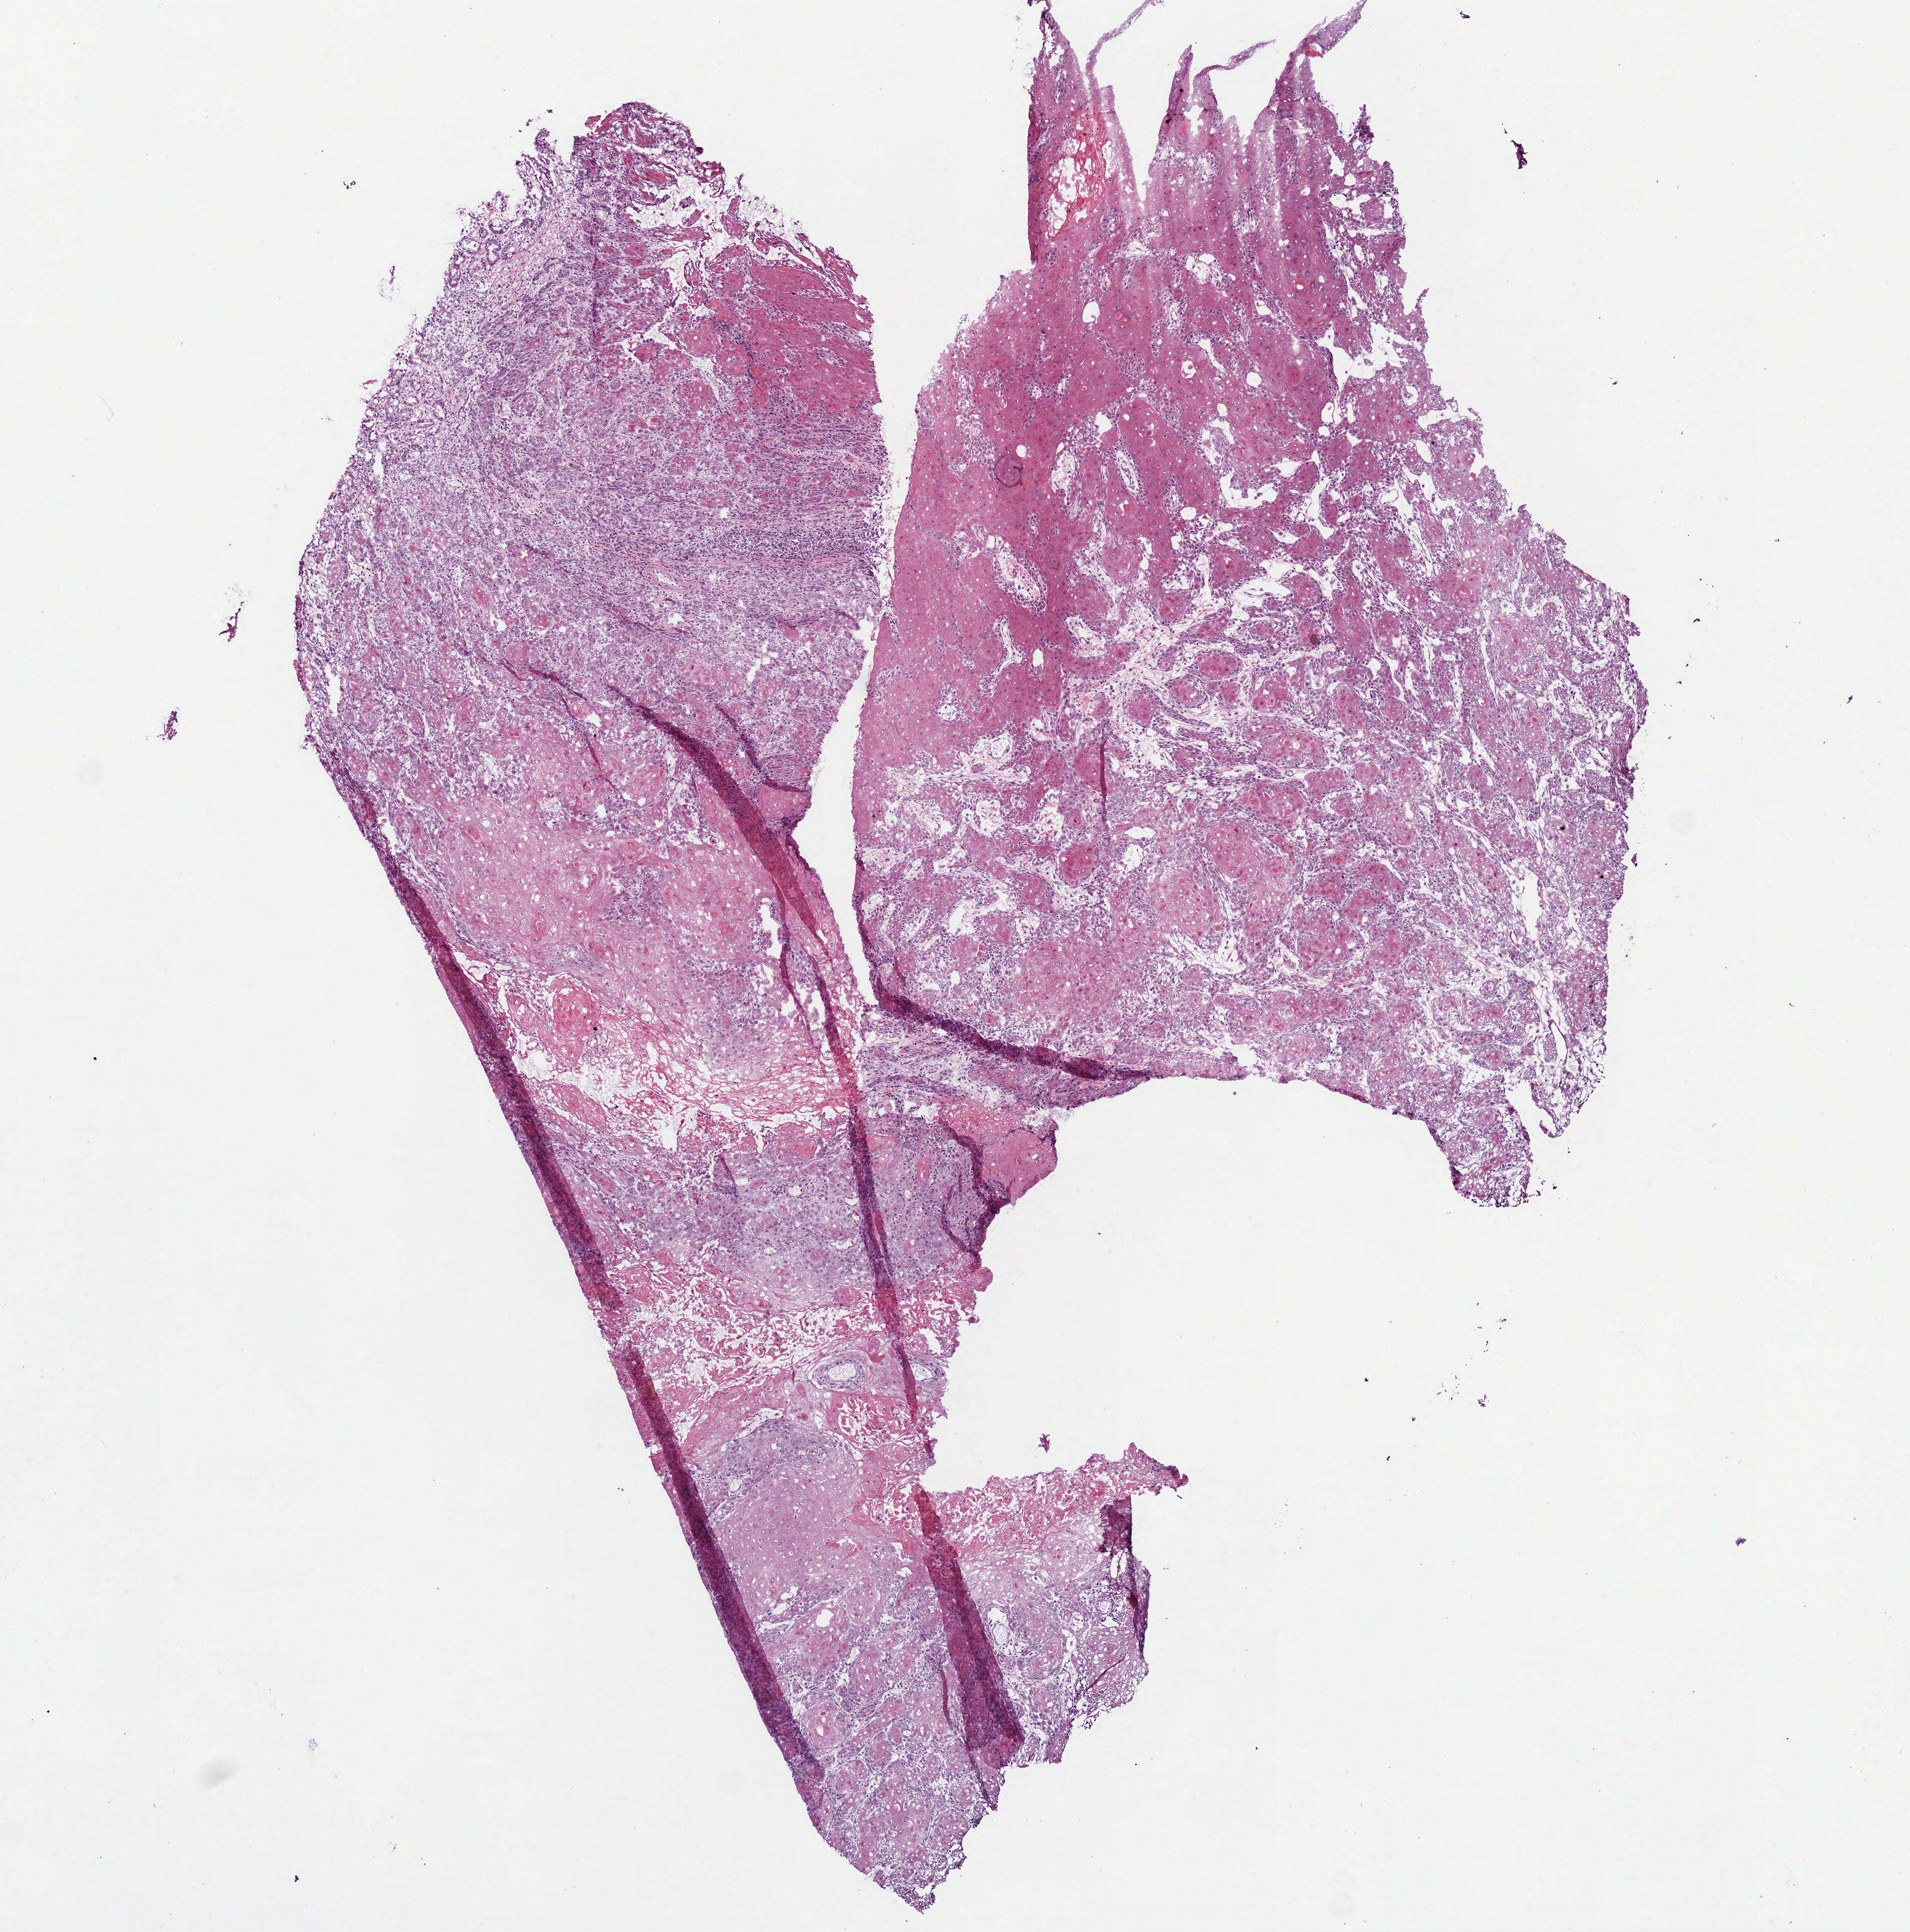
Whole-slide histology image, H&E-stained, low-resolution overview of the scanned area, about 6.0 x 6.1 mm; frozen section; head and neck, primary tumour sample. Female, age 52 years at initial diagnosis. Histologic grade: G2 (moderately differentiated). Pathologist review of this section (percent, as recorded): tumour cells 88%, tumour nuclei 80%, normal cells 0%, stromal cells 12%, necrosis 0%.
AJCC pathologic stage: IVA. Histologic diagnosis: Squamous cell carcinoma, NOS (tongue, NOS).